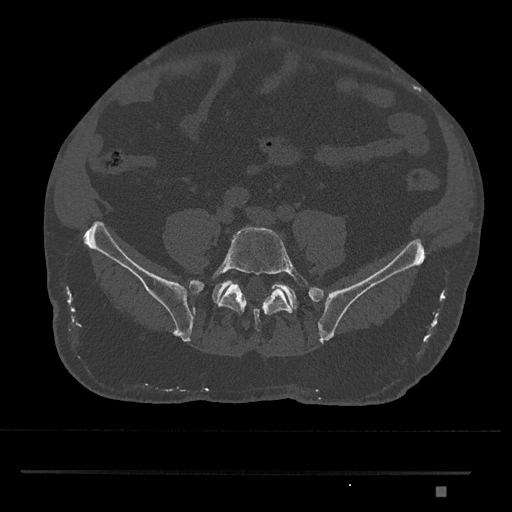
CT including the spine, one axial slice; slice 547 of 1134 in the series (ordered by position); reconstruction kernel Br40s/3; bone window (W 1800 / L 400 HU); 512 × 512 image matrix, field of view 429 × 429 mm. Male patient, age 65 years. Case-level facts recorded for this patient, not image findings: primary cancer: prostate.
Outlined on this slice (semi-automatically segmented with operator editing):
- L5 vertebra: bounding box [x1, y1, x2, y2] px = [210, 227, 311, 332]